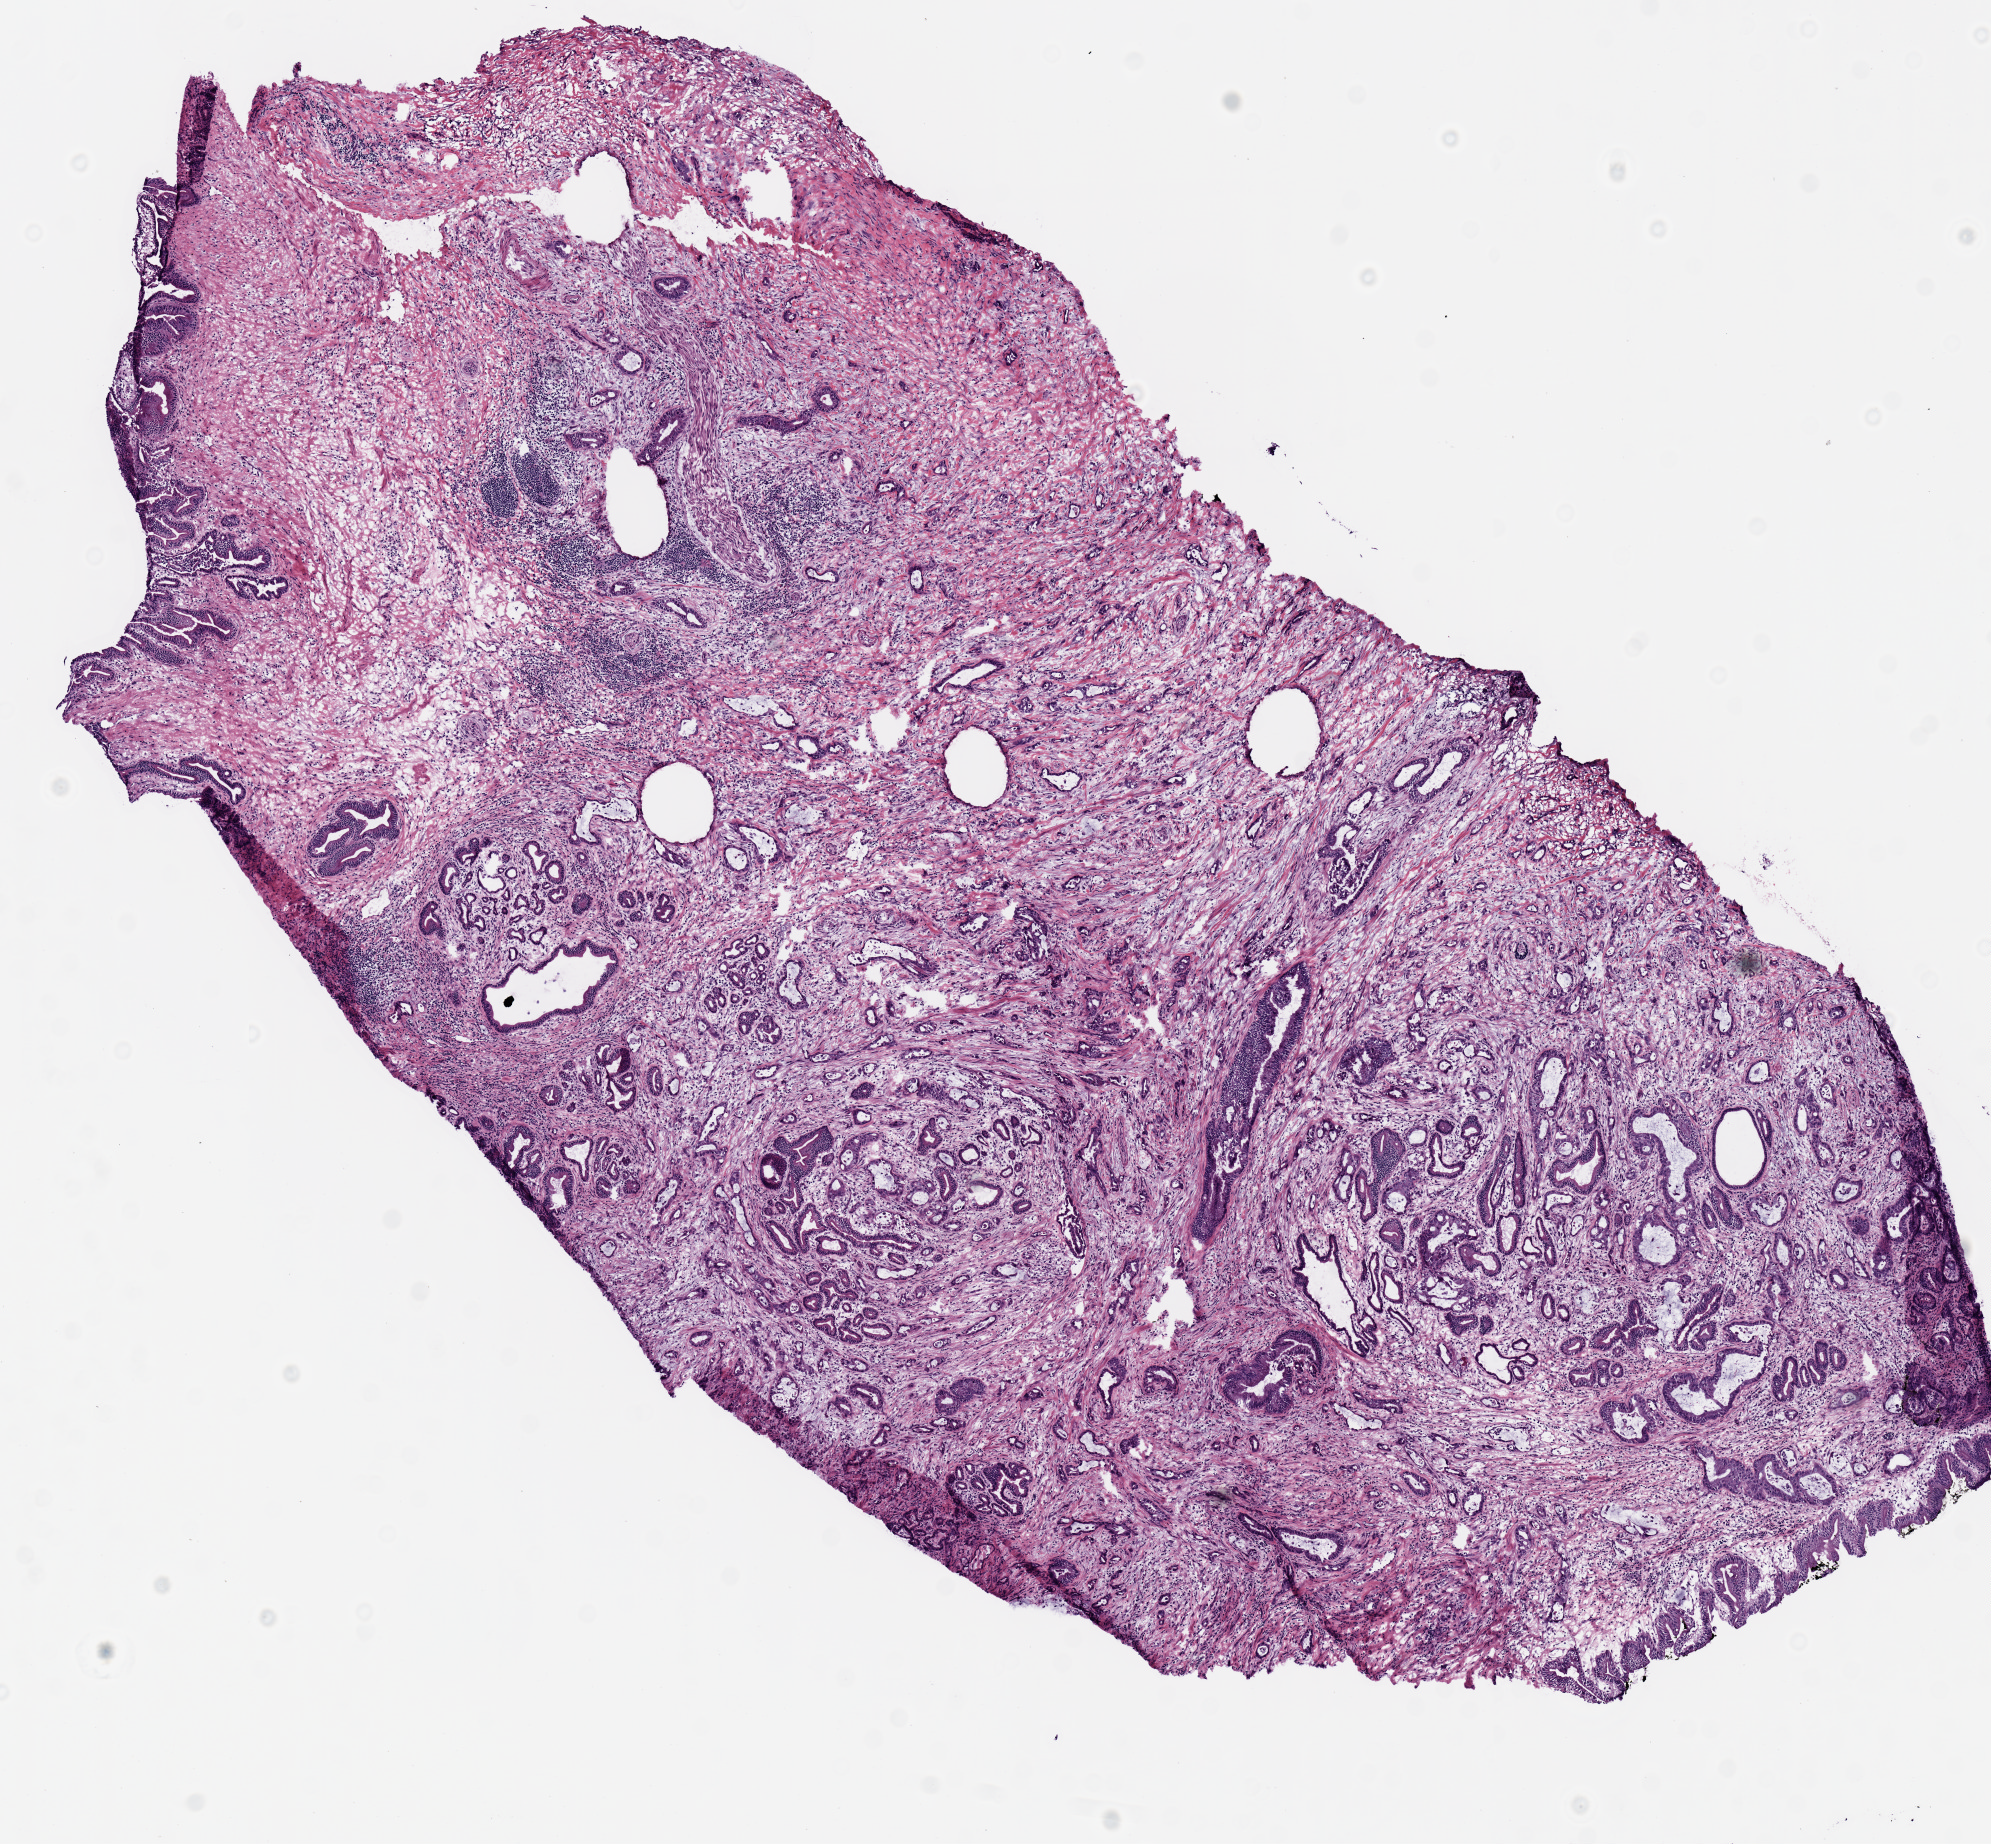
H&E-stained whole-slide image — a low-resolution overview of the entire scanned area, about 7.9 x 7.3 mm. Frozen section from the top of the tissue portion. Sample: primary tumour, pancreas. Patient: male, age at initial diagnosis 57 years. Histologic grade: G1 (well differentiated). Pathologist review of this section (percent, as recorded): tumour nuclei 20%, necrosis 0%.
* diagnosis: Infiltrating duct carcinoma, NOS (head of pancreas)
* lymph nodes positive (case pathology): 2 of 13 examined
* AJCC pathologic stage: IIB